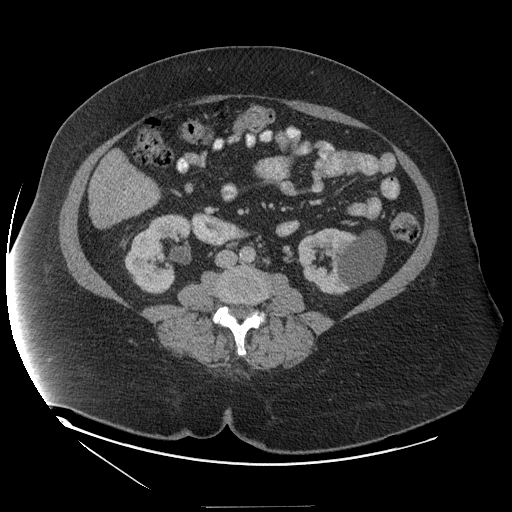
Contrast-enhanced abdominal CT (liver protocol), one axial slice. Position 30 of 127 along the scan axis. Reconstruction kernel STANDARD. Soft-tissue window (W 400 / L 40 HU). 2.5 mm slice thickness. 512 × 512 image matrix, field of view 480 × 480 mm. From the clinical record (not read from this slice): diagnosis: hepatocellular carcinoma (patient treated with transarterial chemoembolisation; whether this scan precedes or follows treatment is not stated here); TNM stage (as recorded): Stage-II; Child-Pugh class: A; tumour nodularity: multinodular; tumour size: 3 cm.
Outlined on this slice (semi-automatic segmentation, software-assisted and operator-edited):
- liver parenchyma outside the tumour (the mass and vessels are separate outlines, so this box may not span the whole liver): box from (x=90, y=200) to (x=127, y=226) px